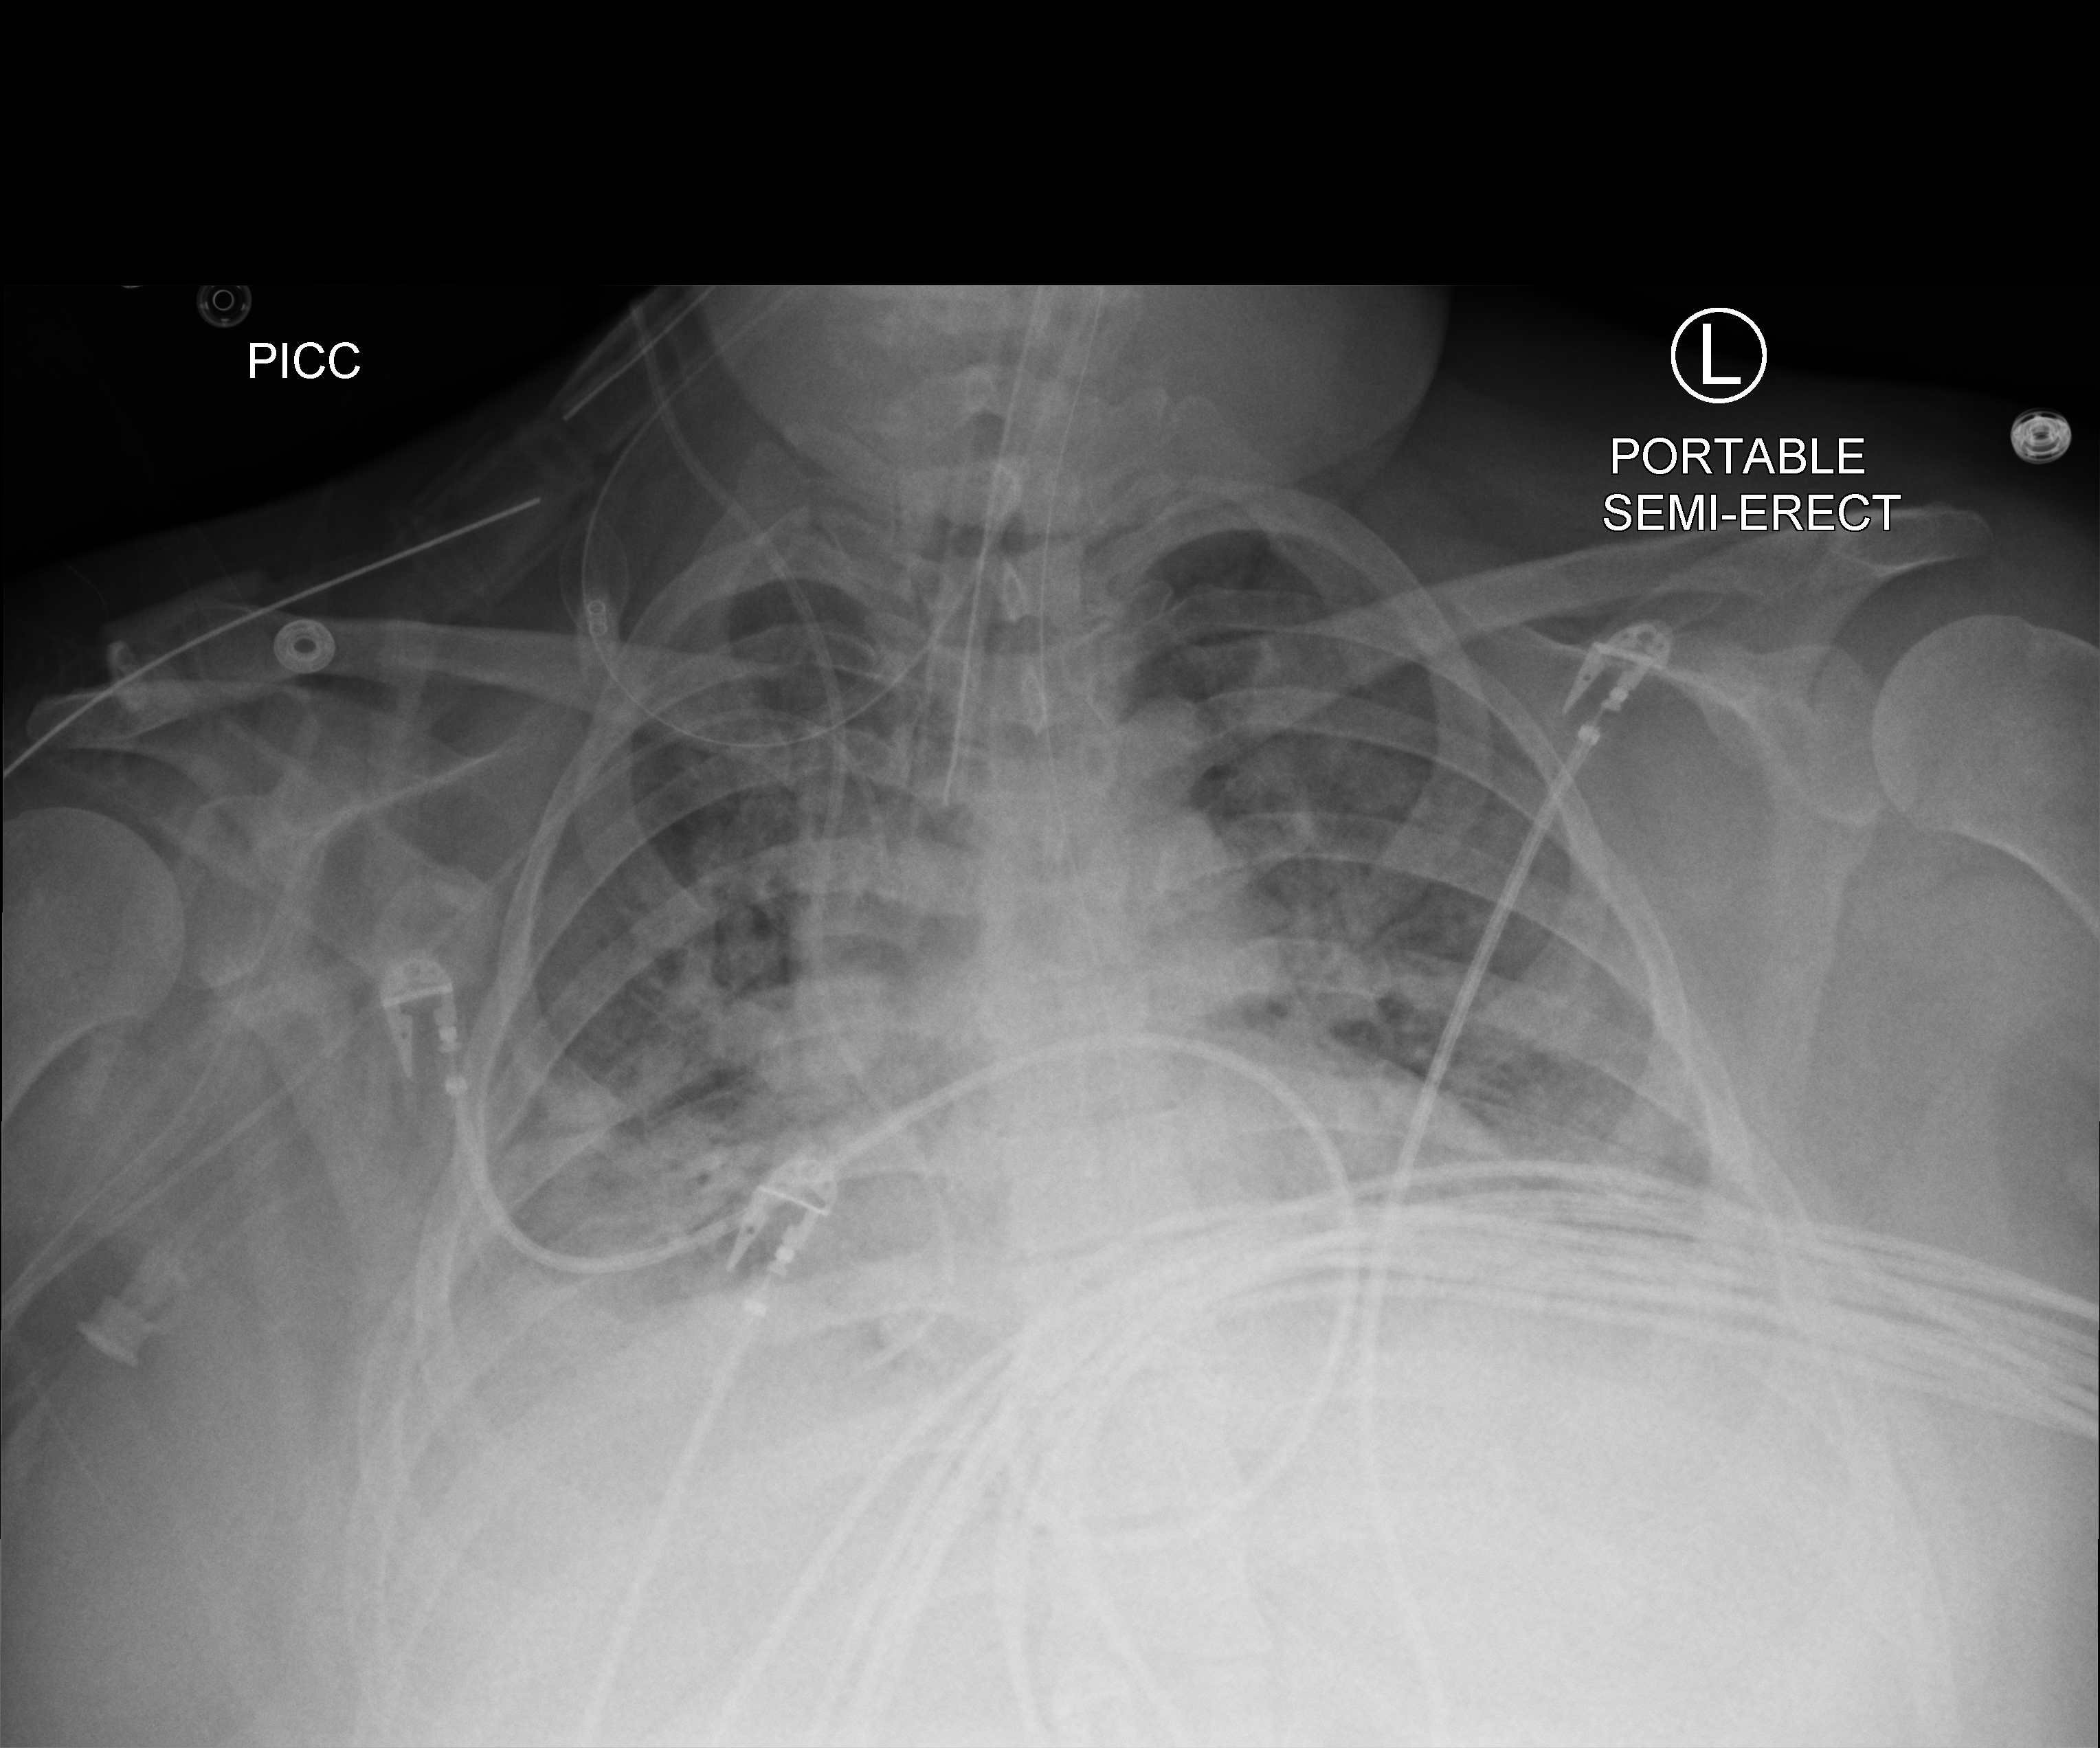
Bedside chest radiograph (computed radiography), anteroposterior (AP) projection. Female patient hospitalised with COVID-19, age 18–59 years.
Hospital-stay facts (about this admission, not read from this image; timing relative to this image not recorded): mechanically ventilated during this hospital stay: yes.